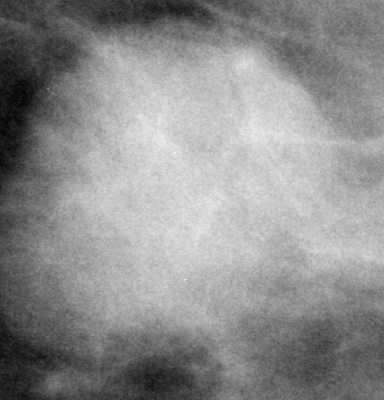
Crop from a digitized film mammogram around one marked abnormality, left breast, CC view, BI-RADS breast density category 2 (scale 1–4).
Mass, shape oval, margins circumscribed; BI-RADS assessment category 4; pathology result (as recorded, not read from the image): malignant.